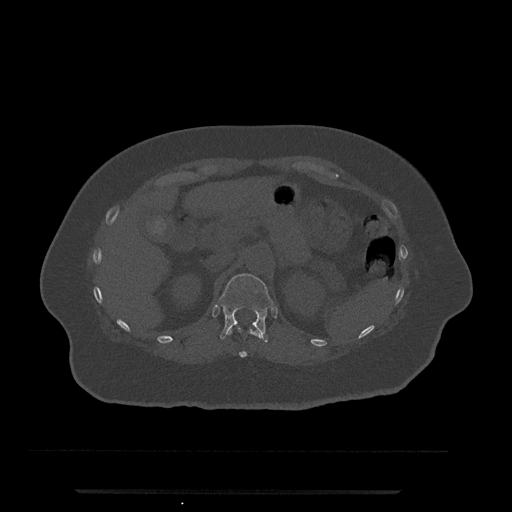
CT including the spine, one axial slice; position 187 of 797 along the scan axis; bone window (W 1800 / L 400 HU); 0.5 mm slice thickness; 512 × 512 image matrix, field of view 440 × 440 mm. Patient: female, 51 years. Case-level facts recorded for this patient, not image findings: primary cancer: neuro; vertebrae with lytic lesions (as recorded): T8.
Annotated regions visible in this slice (semi-automatic segmentation, software-assisted and operator-edited):
- T11 vertebra: box from (x=228, y=326) to (x=261, y=358) px
- T12 vertebra: (x=218, y=274)–(x=274, y=342)